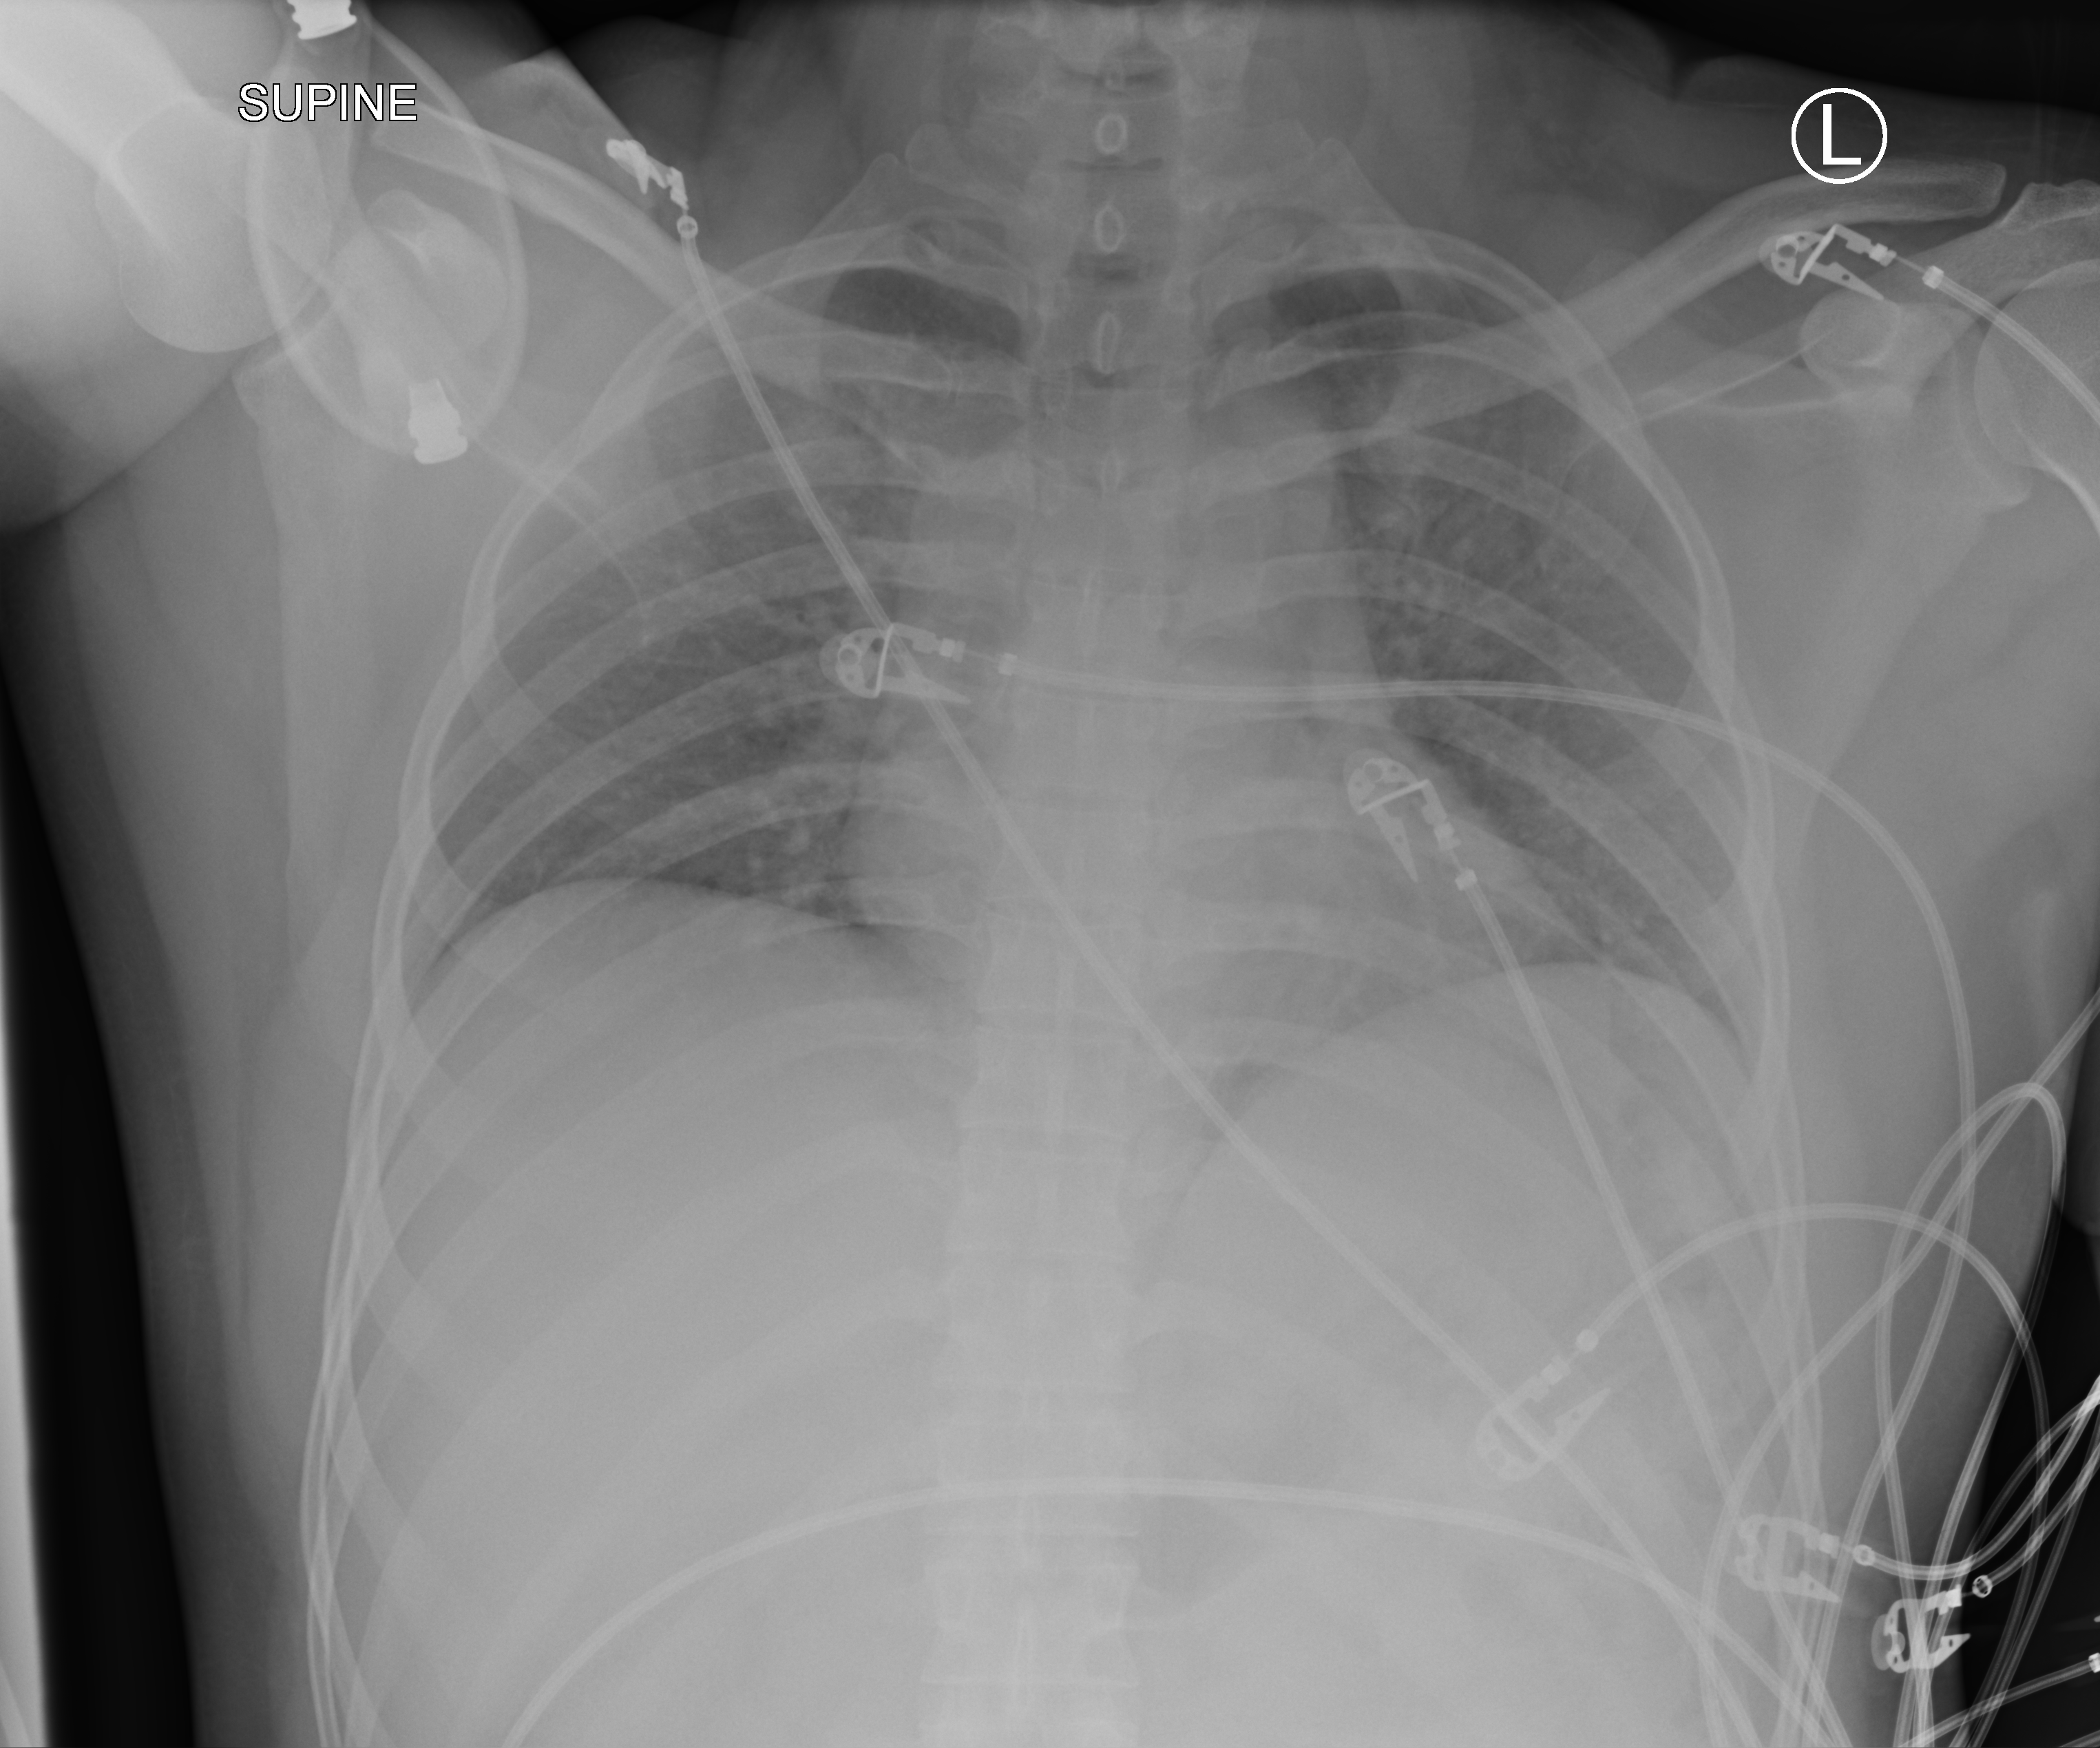
Portable chest radiograph, anteroposterior (AP) projection. Male patient hospitalised with COVID-19, age 18–59 years.
Admission-level facts for this patient (not findings on this image; timing relative to this image not recorded): length of hospital stay: 7 days; admitted to intensive care during this hospital stay: no.